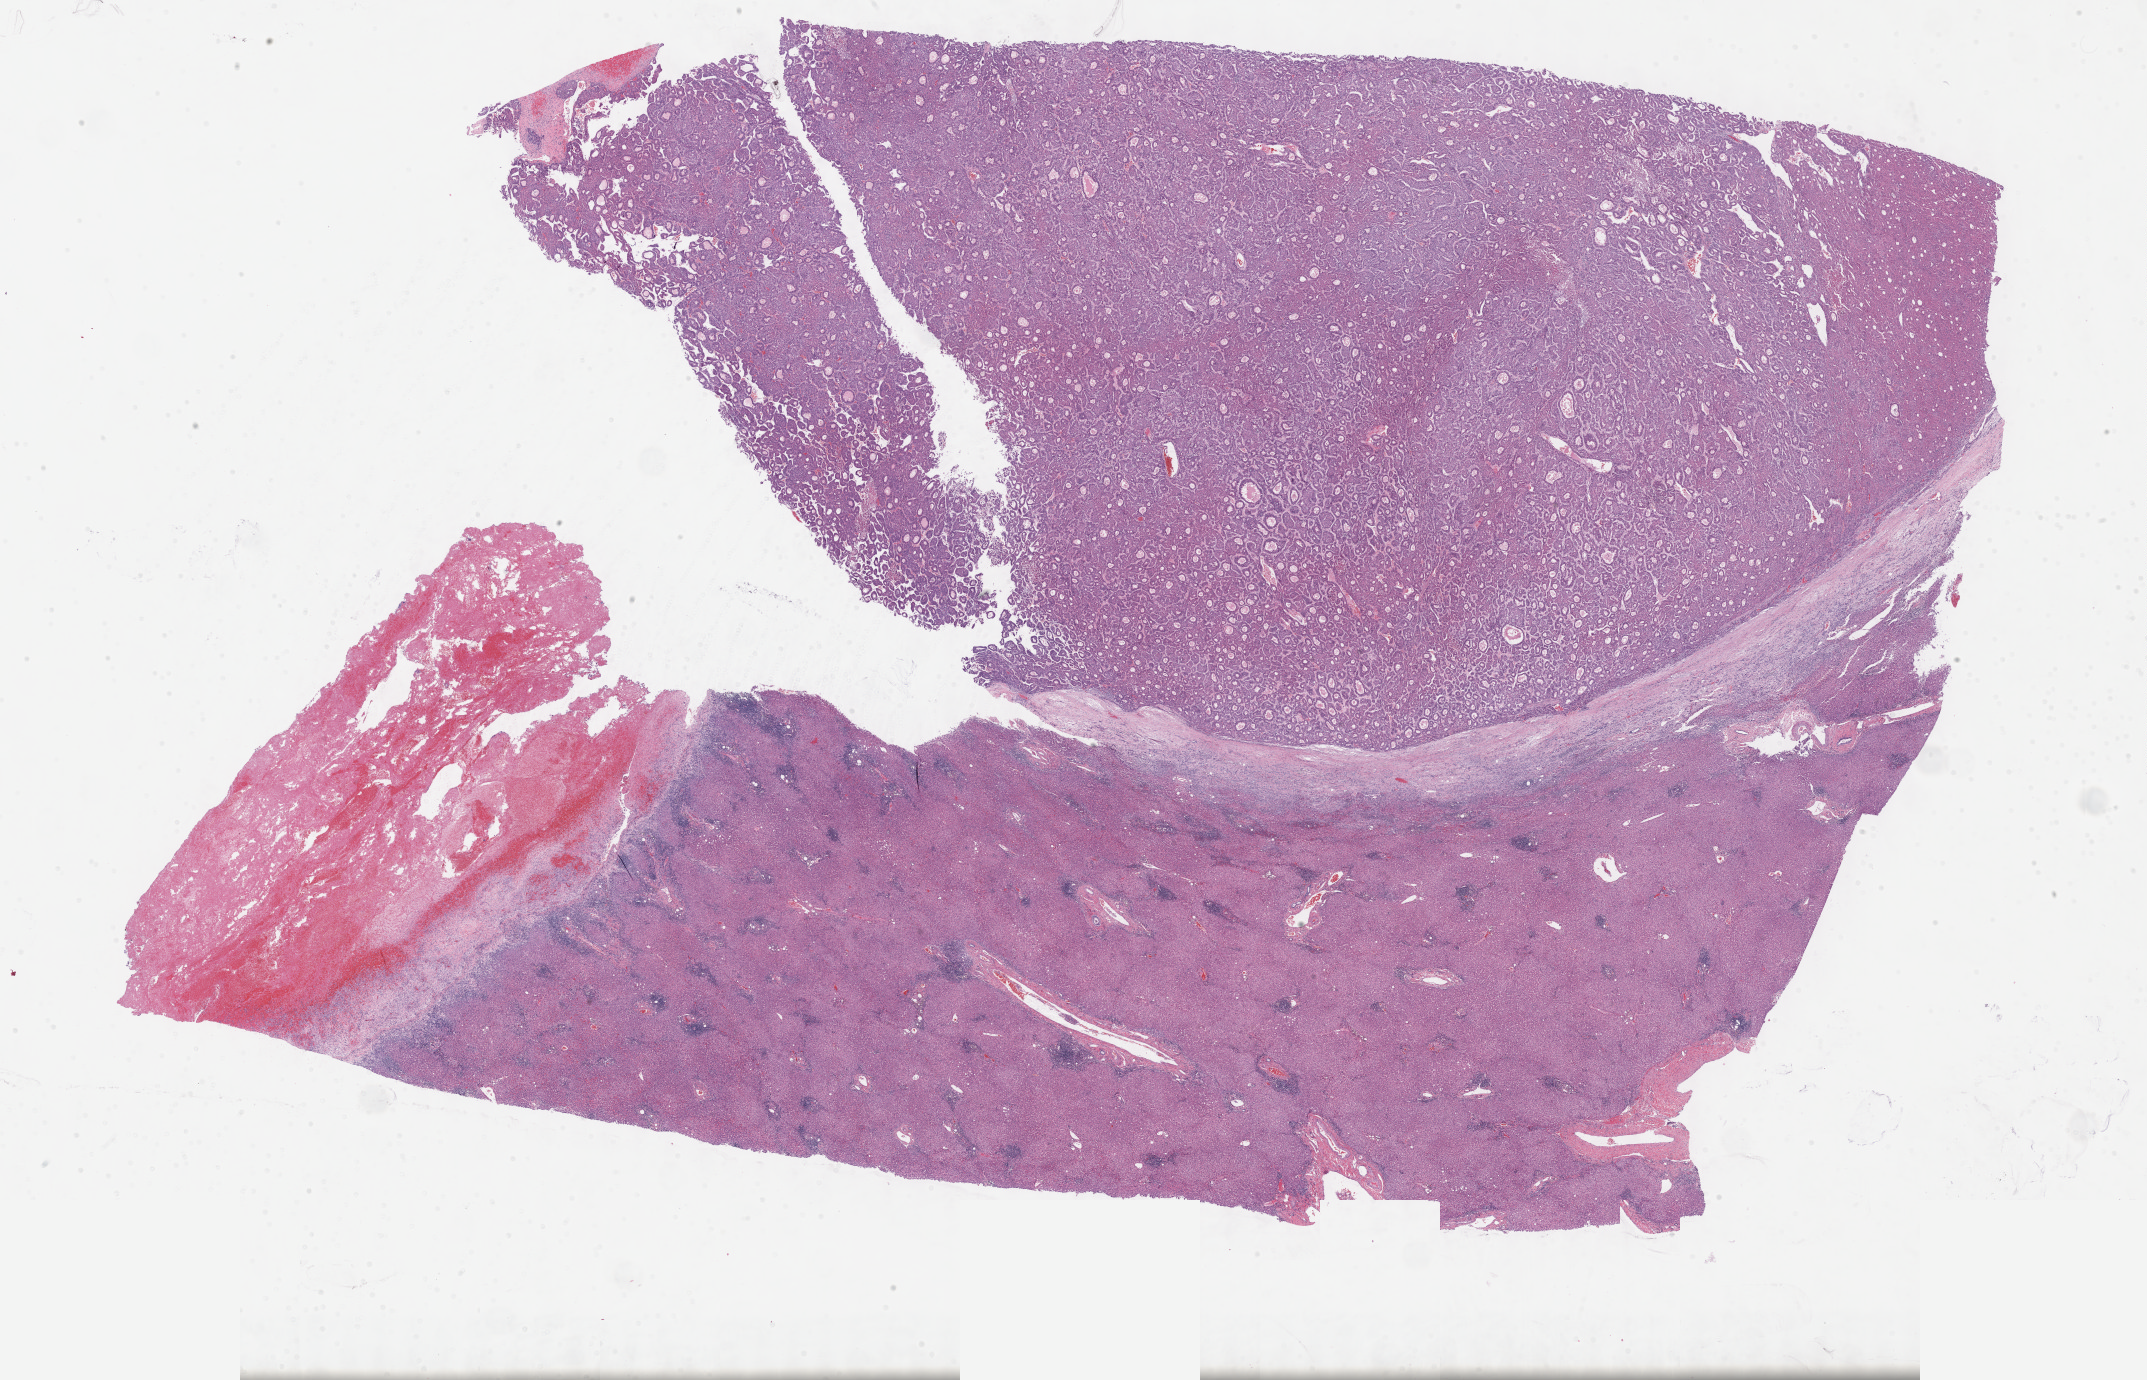
Whole-slide histology image, H&E-stained — a low-resolution overview of the entire scanned area, about 34.7 x 22.3 mm. FFPE section. Liver, primary tumour sample. Male, age 61 years at initial diagnosis. Histologic grade: G2 (moderately differentiated).
- pathologic diagnosis: Hepatocellular carcinoma, NOS
- AJCC pathologic stage: IIIC (7th edition)